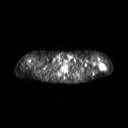
FDG PET of an extremity soft-tissue mass (from a PET/CT study), one axial slice; position 209 of 267 along the scan axis; 128 × 128 image matrix, field of view 600 × 600 mm. Female patient, age 28 years. Case-level facts recorded for this patient, not image findings: histological type: malignant fibrous histiocytoma; grade: low; site of the primary tumour: left arm.
Annotated regions visible in this slice (expert contour drawn on MRI and transferred to this co-registered scan by the dataset authors):
- gross tumour volume (mass): bounding box <98,63,106,70> (left, top, right, bottom; pixels)